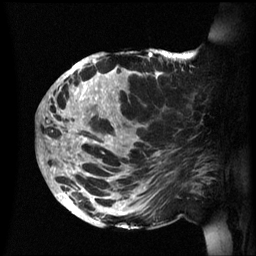
Breast MRI (dynamic contrast-enhanced), one sagittal slice. Position 29 of 60 along the scan axis. Dynamic contrast-enhanced series, image 2 of 3 at this slice position (ordered by acquisition). 1.5 T. TE 4.2 ms, TR 8.4 ms. 256 × 256 image matrix. Patient: female, 48 years.
Structures marked on this image (semi-automatically segmented with operator editing):
- analysis volume of interest (the breast-tissue region the enhancement analysis was run in; not a lesion): bounding box <42,49,202,230> (left, top, right, bottom; pixels)
- tumour enhancement mask (voxels above the 70 % enhancement threshold inside the analysis volume of interest): <42,52,162,224>